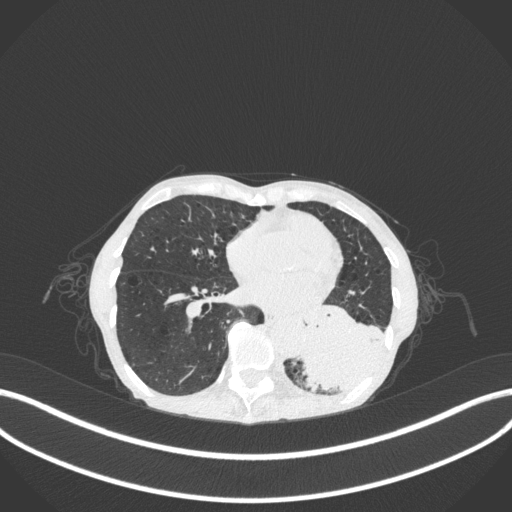
Chest CT, one axial slice. Slice 101 of 347 in the series (ordered by position). Reconstruction kernel B31f. 120 kVp. Lung window (W 1500 / L -600 HU). 1 mm slice thickness. 512 × 512 image matrix, field of view 400 × 400 mm. Female patient, age 70 years. Case-level facts recorded for this patient, not image findings: clinical TNM (as recorded): T3 N0 M0.
Annotated regions visible in this slice (bounding box drawn by a radiologist):
- lung tumour (recorded histology: small cell carcinoma): bounding box [x1, y1, x2, y2] px = [292, 290, 390, 397]